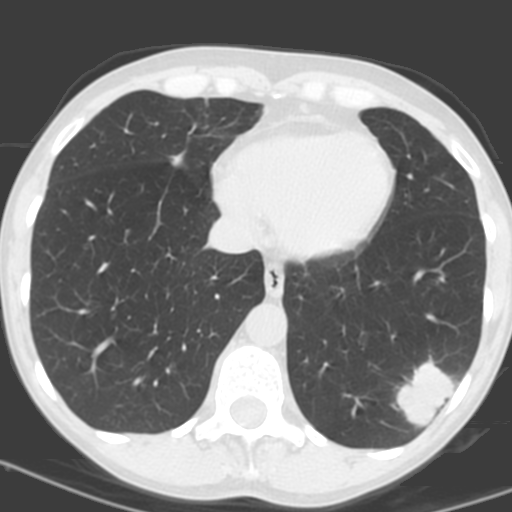
Axial slice from a low-dose chest CT screening exam. First (baseline) screen. Lung window (W 1500 / L -600 HU). Standard (soft-tissue) reconstruction kernel (C). 120 kVp. 512 × 512 image matrix, field of view 262 × 262 mm. Female participant, aged 56 years at enrolment.
Expert reader's lesion annotation, box from (x=387, y=358) to (x=464, y=427) px. Reader record for this screening exam (exam-level; its link to the box is not recorded): non-calcified nodule or mass ≥4 mm, left lower lobe, 31 × 23 mm, poorly defined margins, soft tissue attenuation, pre-existing on the prior screen: no. Lung cancer was diagnosed 27 days after this screen: squamous cell carcinoma, NOS, left lower lobe, poorly differentiated (G3), stage IB (AJCC 6th edition), 35 mm at pathology.